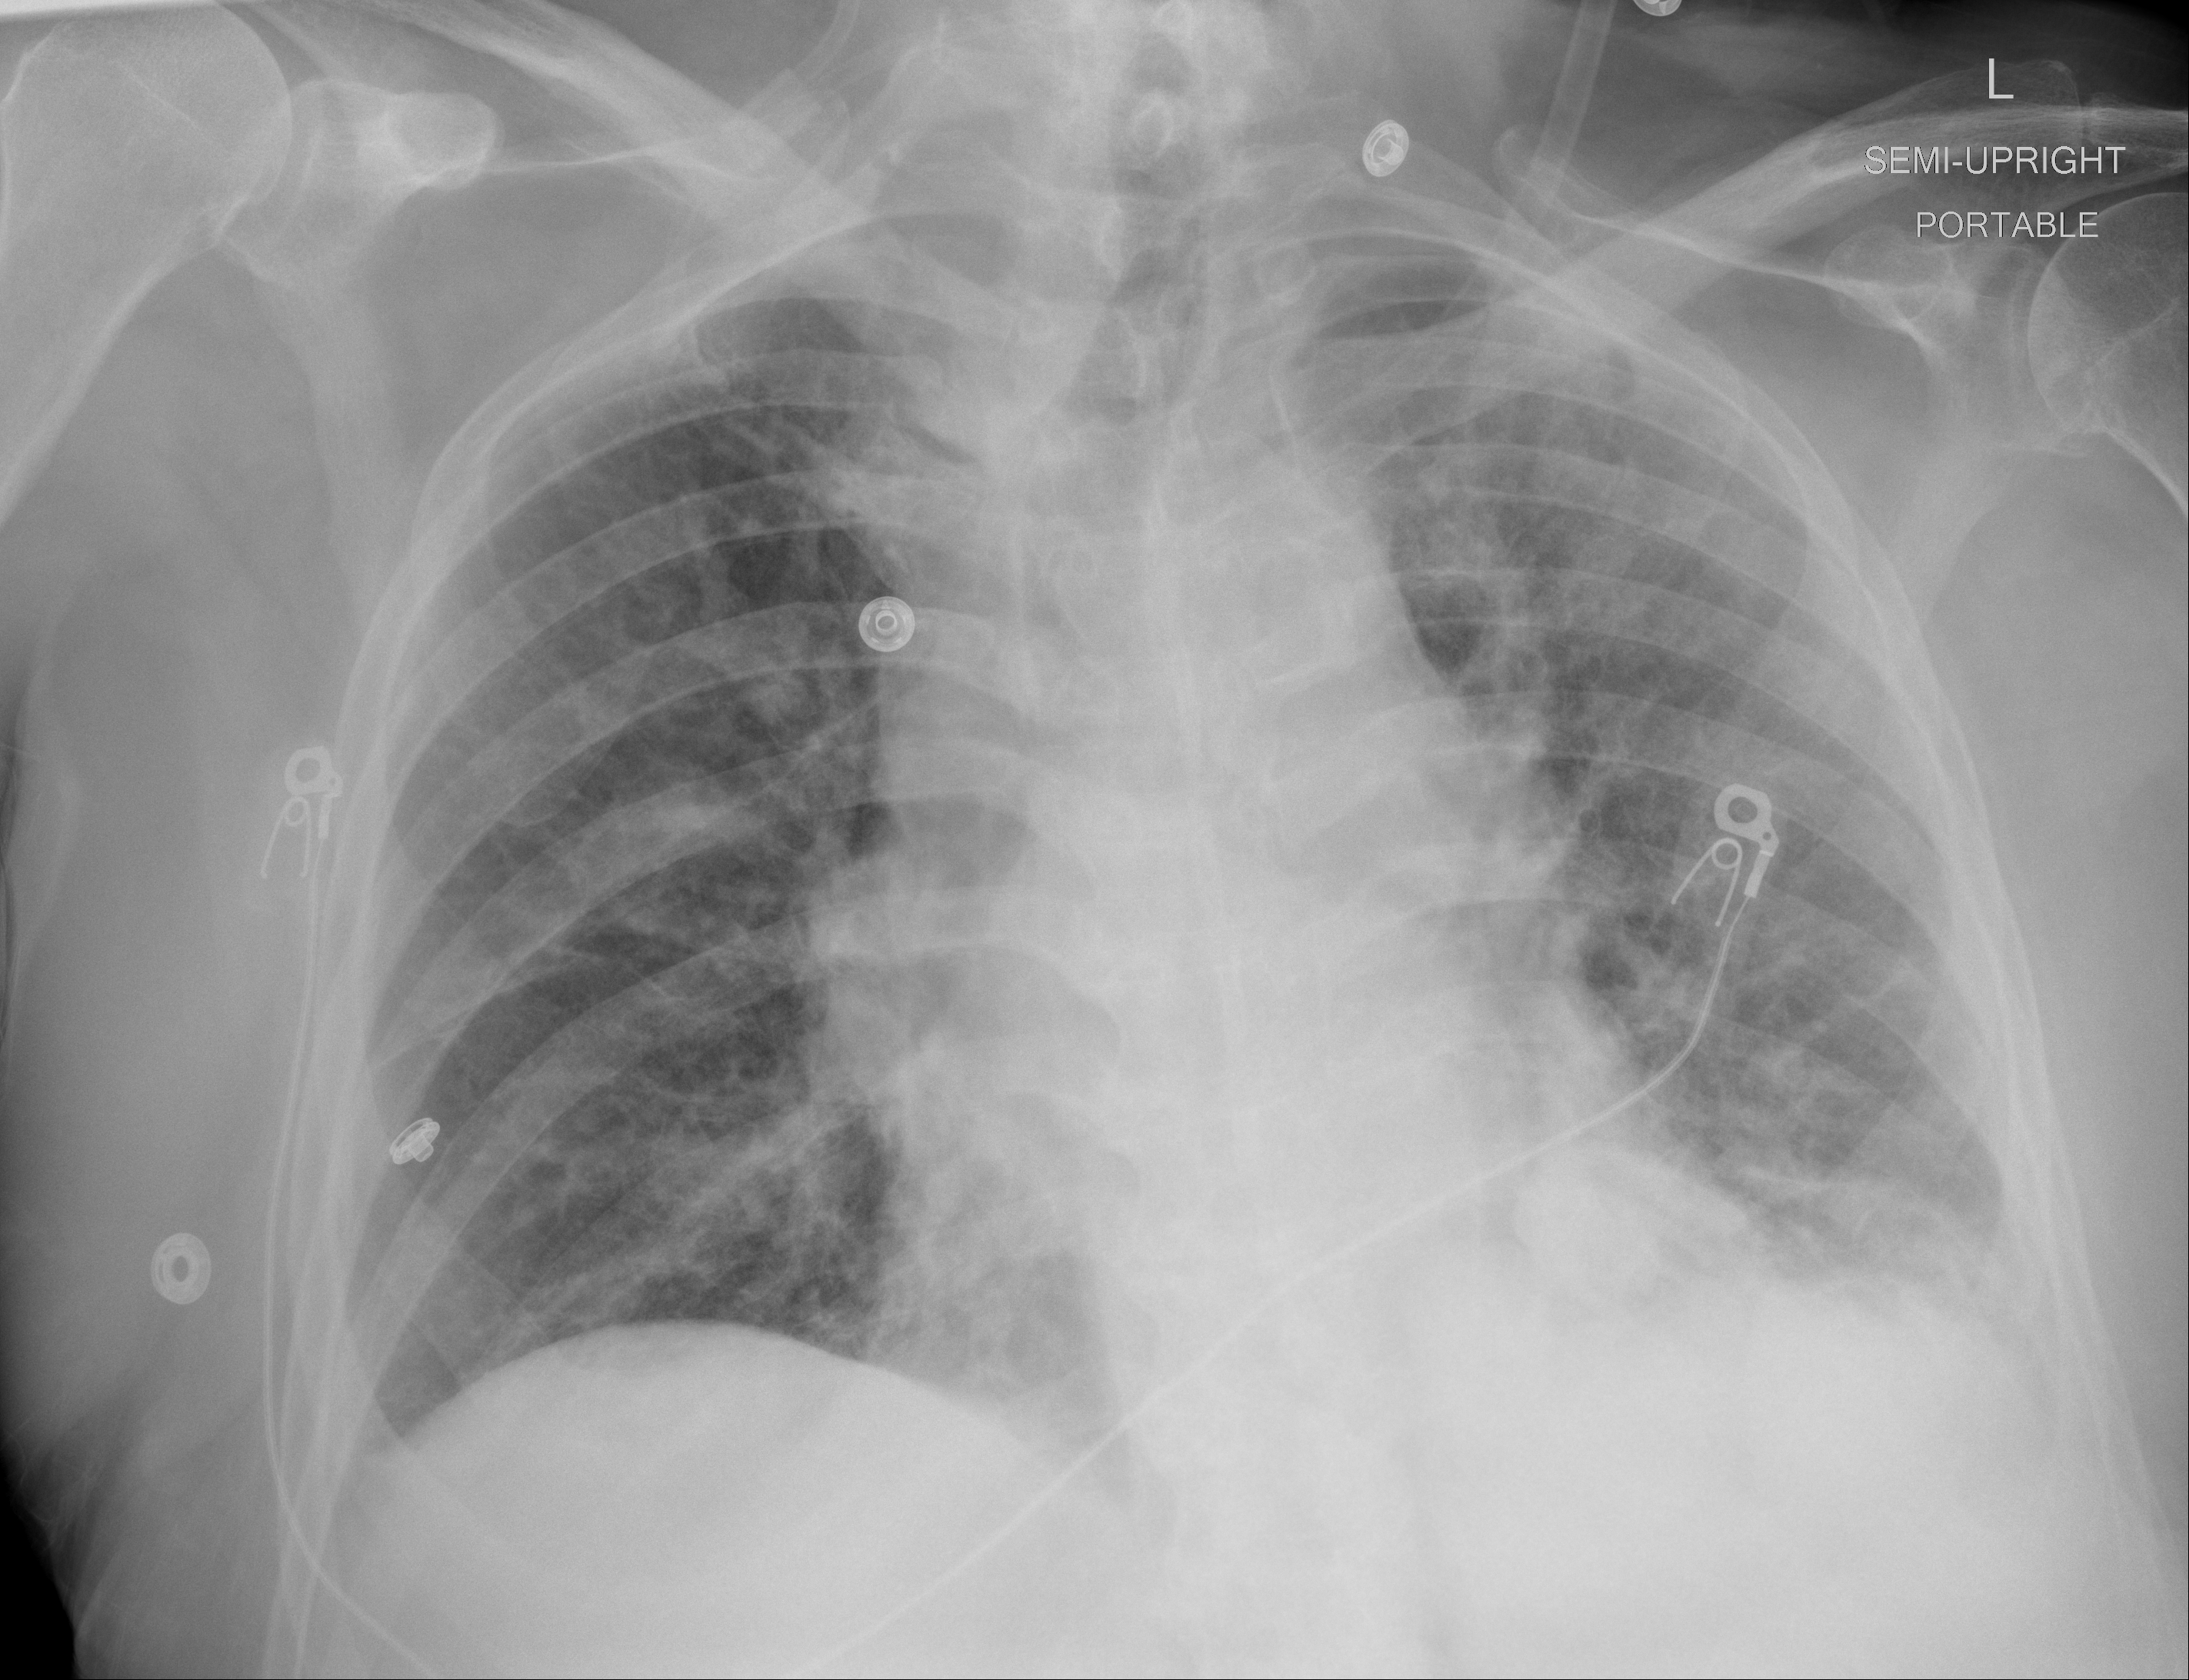
Portable chest radiograph, AP projection. Male patient, age 89 years; imaged 12 days after the COVID-19 diagnosis.
Key findings recorded by the radiologist: airspace disease in left mid lung appears largely unchanged.